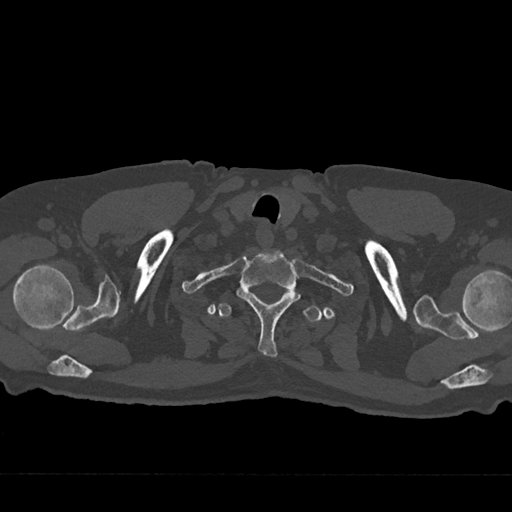
CT including the spine, one axial slice; position 652 of 797 along the scan axis; reconstruction kernel Br40s/3; 120 kVp; bone window (W 1800 / L 400 HU); 0.5 mm slice thickness; 512 × 512 image matrix. Patient: male, 75 years. From the clinical record (not read from this slice): primary cancer: renal.
Outlined on this slice (semi-automatically segmented with operator editing):
- T1 vertebra: bounding box [x1, y1, x2, y2] px = [236, 250, 299, 357]
- T2 vertebra: [218, 289, 322, 323]